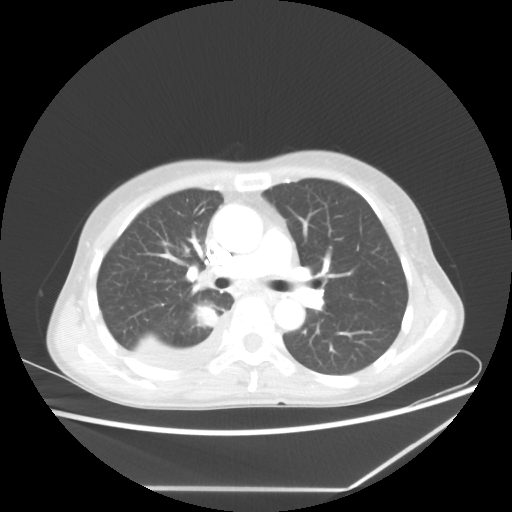
Chest CT, one axial slice. Slice 36 of 60 in the series (ordered by position). Lung window (W 1500 / L -600 HU). 5 mm slice thickness. 512 × 512 image matrix, field of view 364 × 364 mm. Patient: female, 59 years. Case-level facts recorded for this patient, not image findings: clinical TNM (as recorded): T1c N1 M1.
Outlined on this slice (rectangle marked by the reading radiologist):
- lung tumour (recorded histology: adenocarcinoma): box from (x=194, y=303) to (x=219, y=333) px